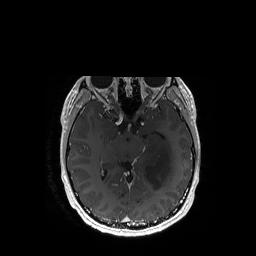
Brain MRI from a brain-tumour surgery series, one axial slice; position 101 of 192 along the scan axis; T1-weighted post-contrast; 1 mm slice thickness; 256 × 256 image matrix. Case-level facts recorded for this patient, not image findings: histopathology: Astrocytoma; WHO grade: 3; IDH mutation: yes; tumour location: Left Temporal.
Structures marked on this image (expert manual segmentation):
- tumour: box from (x=145, y=143) to (x=173, y=189) px